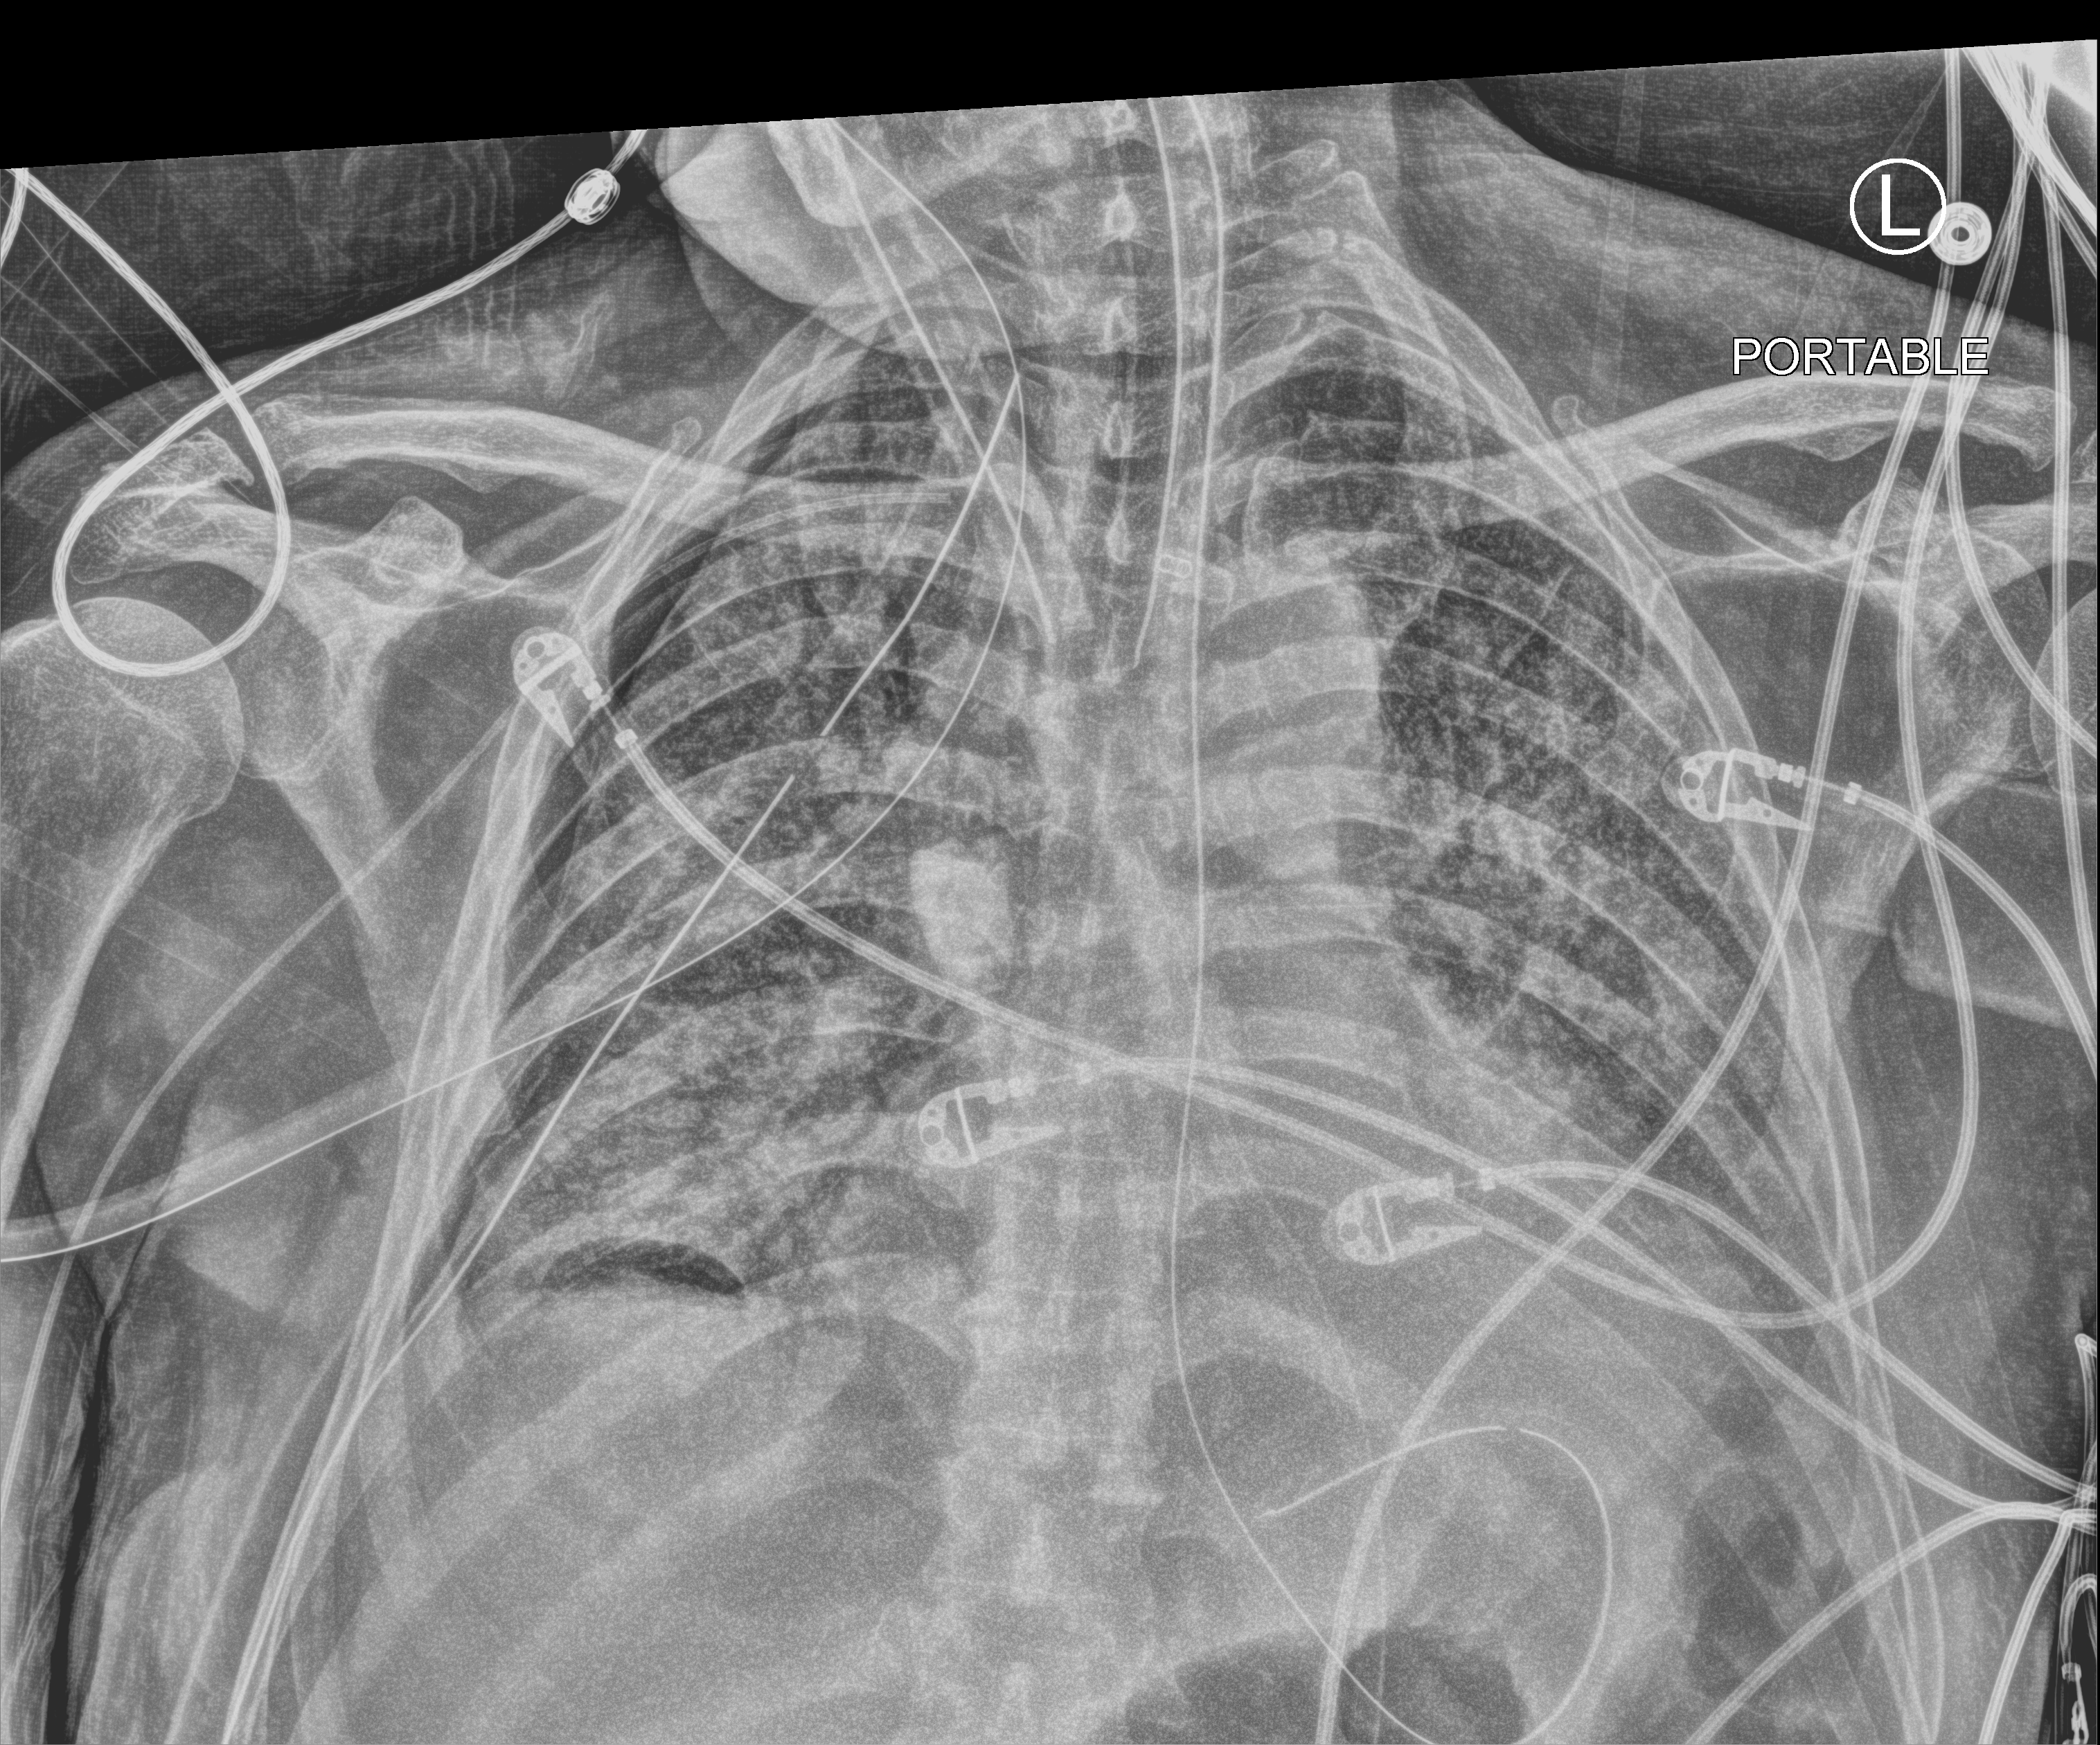
Bedside chest radiograph (computed radiography). Patient hospitalised with COVID-19; male, aged 60–74 years.
Hospital-stay facts (about this admission, not read from this image; timing relative to this image not recorded): admitted to intensive care during this hospital stay: yes.